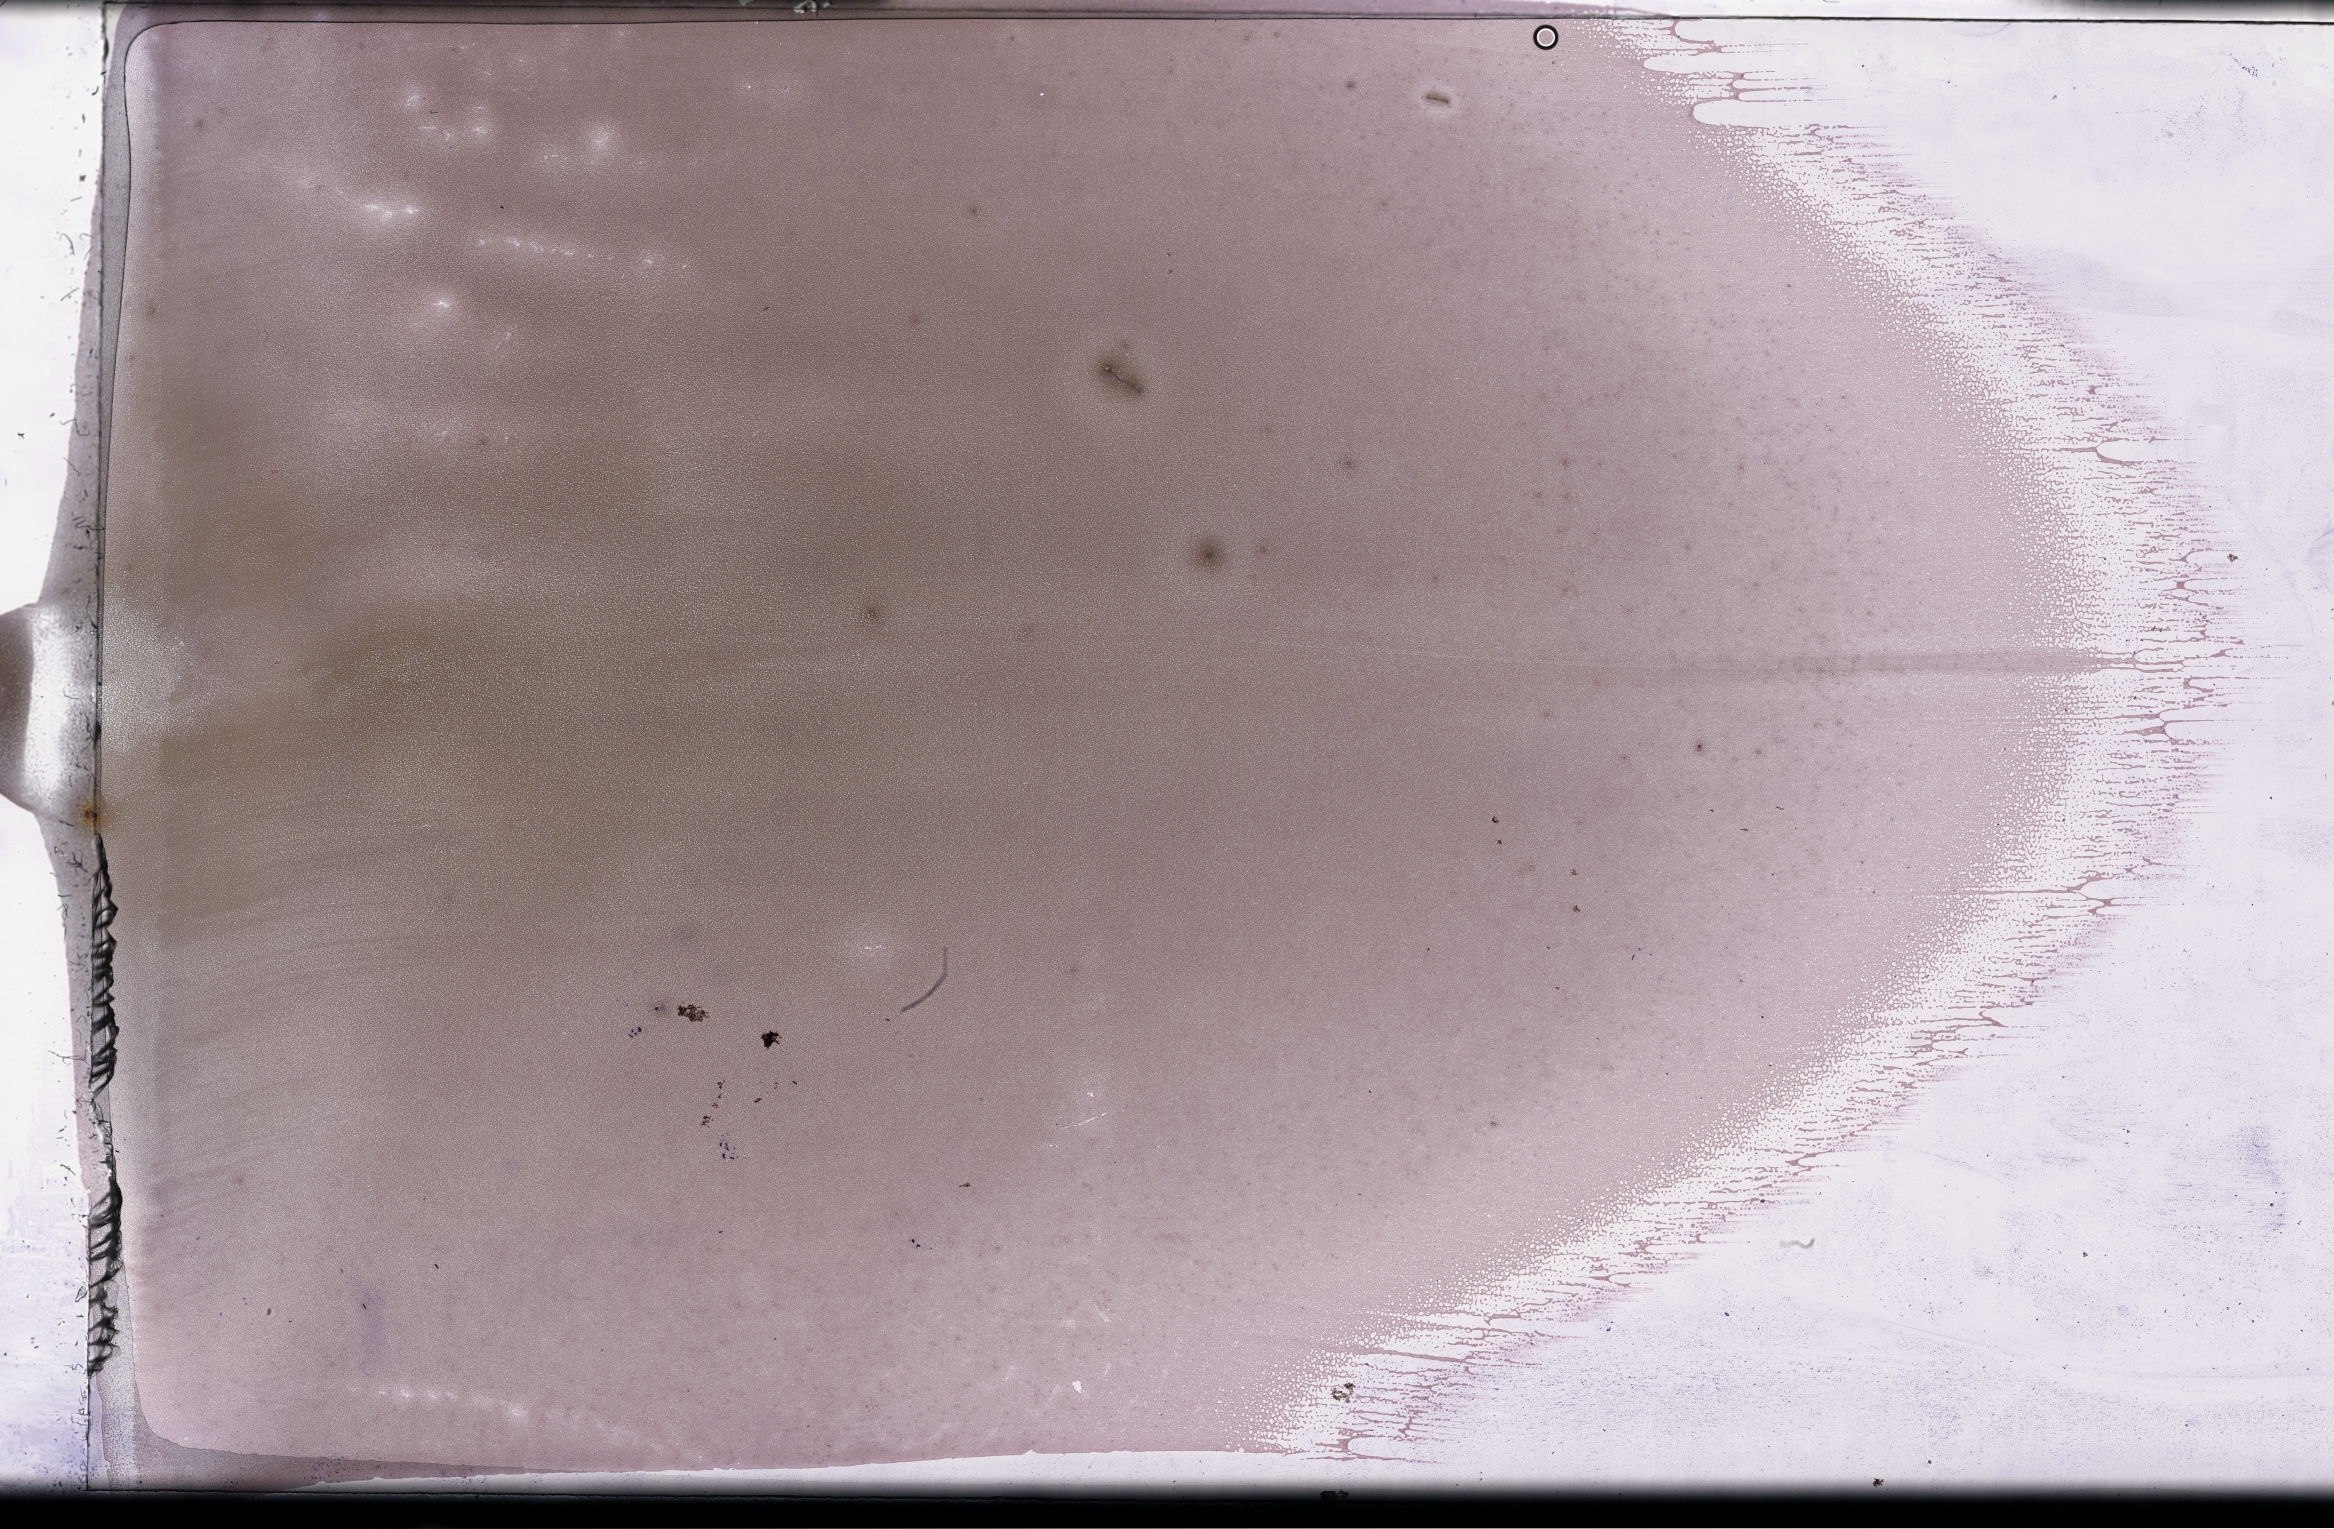
Wright-Giemsa-stained whole blood smear, whole-slide image, shown as a low-resolution overview of the whole scanned area (about 37.7 x 24.7 mm). Smear from an EDTA sample. Collected on treatment. Patient: male.
* patient diagnosis: Plasma Cell Myeloma